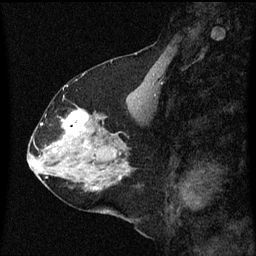
Breast MRI (dynamic contrast-enhanced), one sagittal slice; slice 25 of 60 in the series (ordered by position); dynamic contrast-enhanced series, image 2 of 3 at this slice position (ordered by acquisition); 1.5 T; TE 4.2 ms, TR 8 ms; 2 mm slice thickness; 256 × 256 image matrix, field of view 200 × 200 mm. Female patient, age 58 years.
Annotated regions visible in this slice (semi-automatic segmentation, software-assisted and operator-edited):
- analysis volume of interest (the breast-tissue region the enhancement analysis was run in; not a lesion): box from (x=56, y=110) to (x=99, y=149) px
- tumour enhancement mask (voxels above the 70 % enhancement threshold inside the analysis volume of interest): (x=59, y=110)–(x=90, y=147)